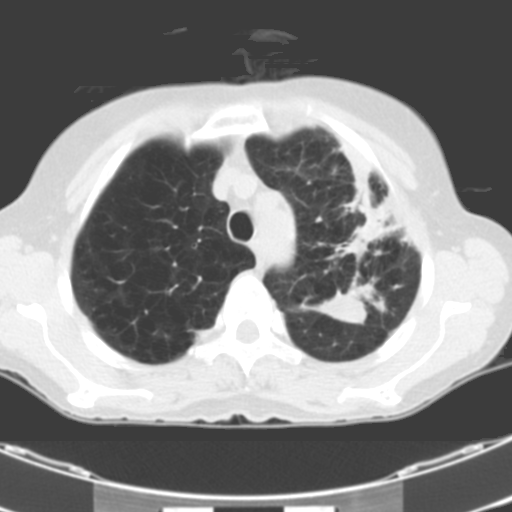
Low-dose screening chest CT, one axial slice. Slice 83 of 106 in the series (ordered by position). 120 kVp. One of 2 acquisitions stored at this slice position. Lung window (W 1500 / L -600 HU). 512 × 512 image matrix, field of view 299 × 299 mm.
Outlined on this slice (manually delineated by an expert):
- lesion 1 (tumor): bounding box [x1, y1, x2, y2] px = [319, 290, 367, 324]